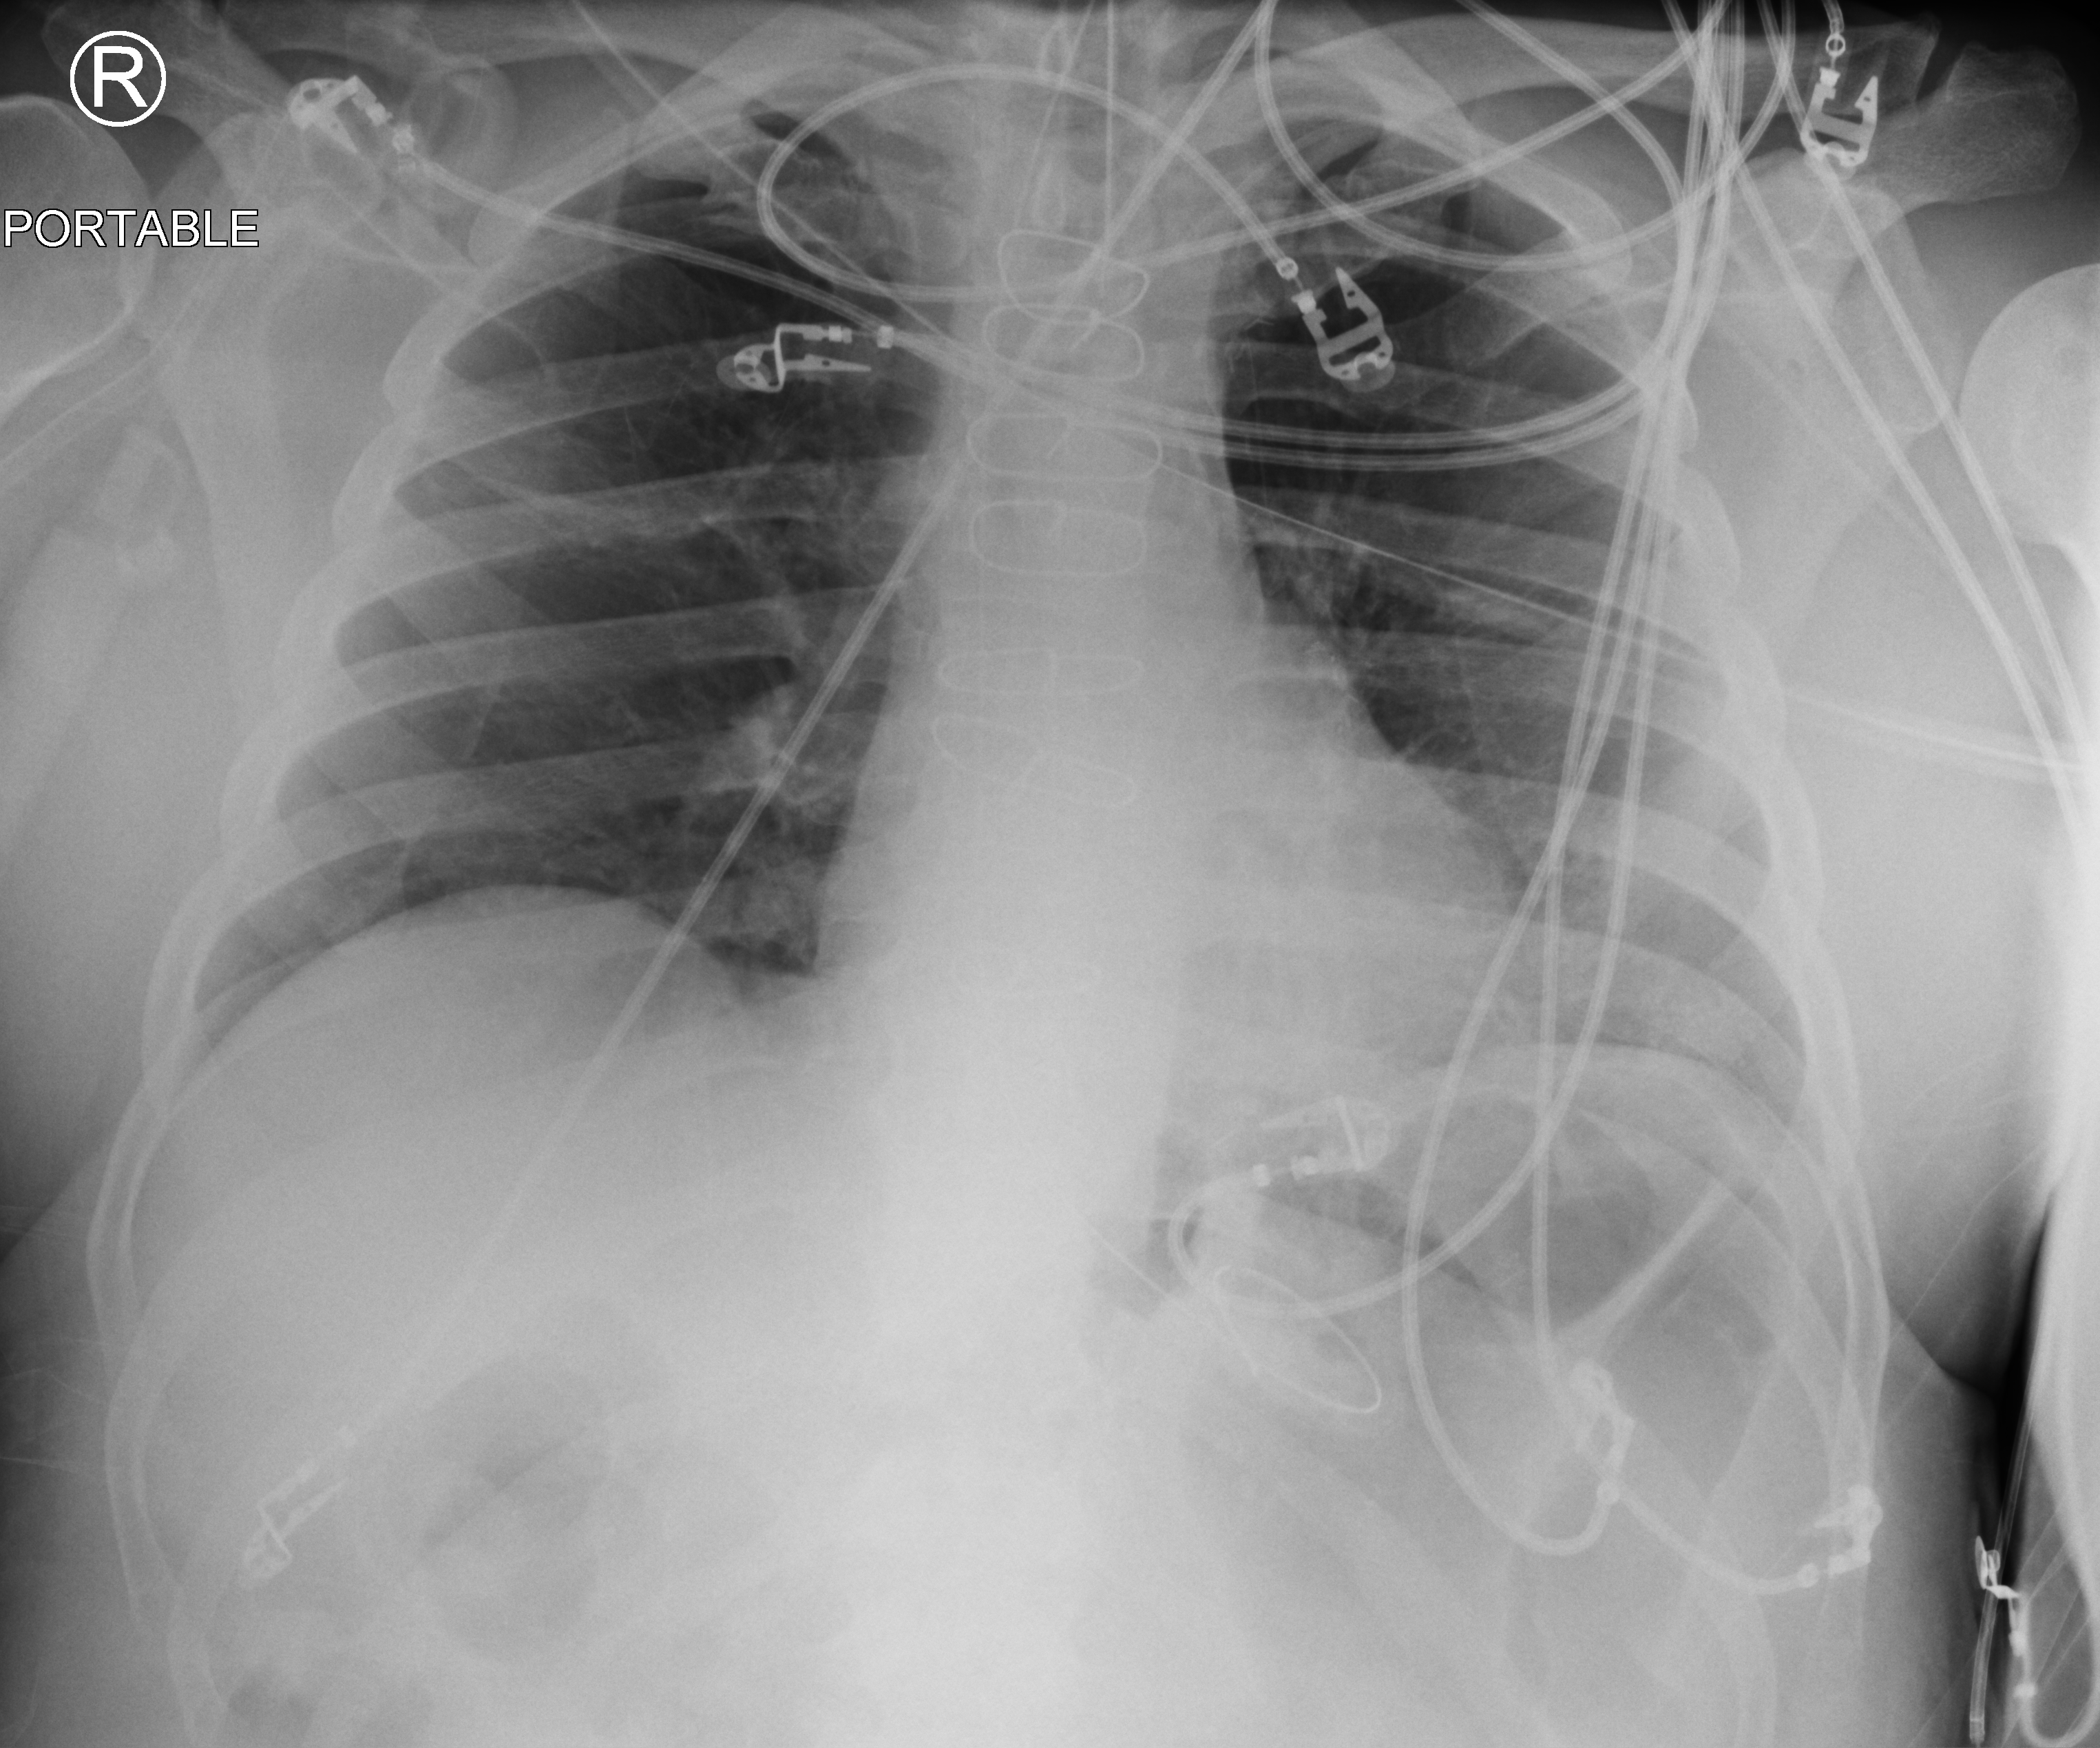
Bedside chest radiograph (computed radiography); anteroposterior (AP) projection. Male patient hospitalised with COVID-19, age 60–74 years.
Admission-level facts for this patient (not findings on this image; timing relative to this image not recorded):
- hypertension (admission record): yes
- mechanically ventilated during this hospital stay: yes
- length of hospital stay: 44 days